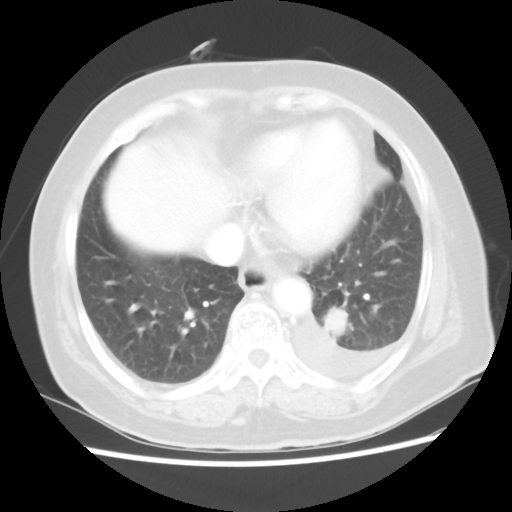
Chest CT, one axial slice. Slice 18 of 80 in the series (ordered by position). 100 kVp. Lung window (W 1500 / L -600 HU). 5 mm slice thickness. 512 × 512 image matrix, field of view 343 × 343 mm. Patient: female, 68 years. From the clinical record (not read from this slice): clinical TNM (as recorded): T1c N0 M1.
Annotated regions visible in this slice (rectangle marked by the reading radiologist):
- lung tumour (recorded histology: adenocarcinoma): bounding box (x1, y1, x2, y2) in pixels: (318, 305, 355, 342)